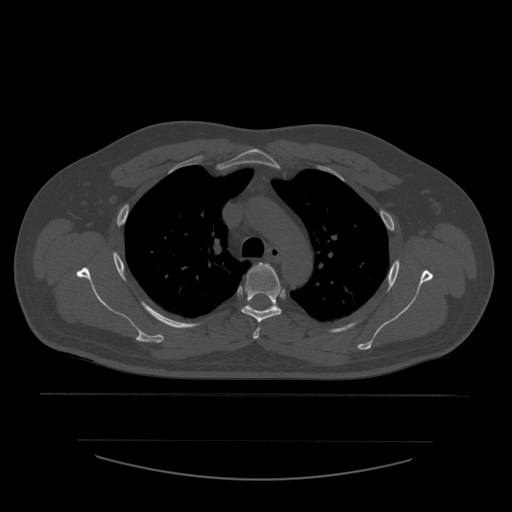
CT including the spine, one axial slice; position 418 of 532 along the scan axis; reconstruction kernel STANDARD; bone window (W 1800 / L 400 HU); 1.25 mm slice thickness; 512 × 512 image matrix, field of view 441 × 441 mm. Patient age 44 years. From the clinical record (not read from this slice): primary cancer: soft tissue sarcoma.
Structures marked on this image (semi-automatically segmented with operator editing):
- T3 vertebra: bounding box (x1, y1, x2, y2) in pixels: (253, 320, 261, 339)
- T4 vertebra: (242, 263, 282, 322)
- T5 vertebra: (247, 304, 277, 308)